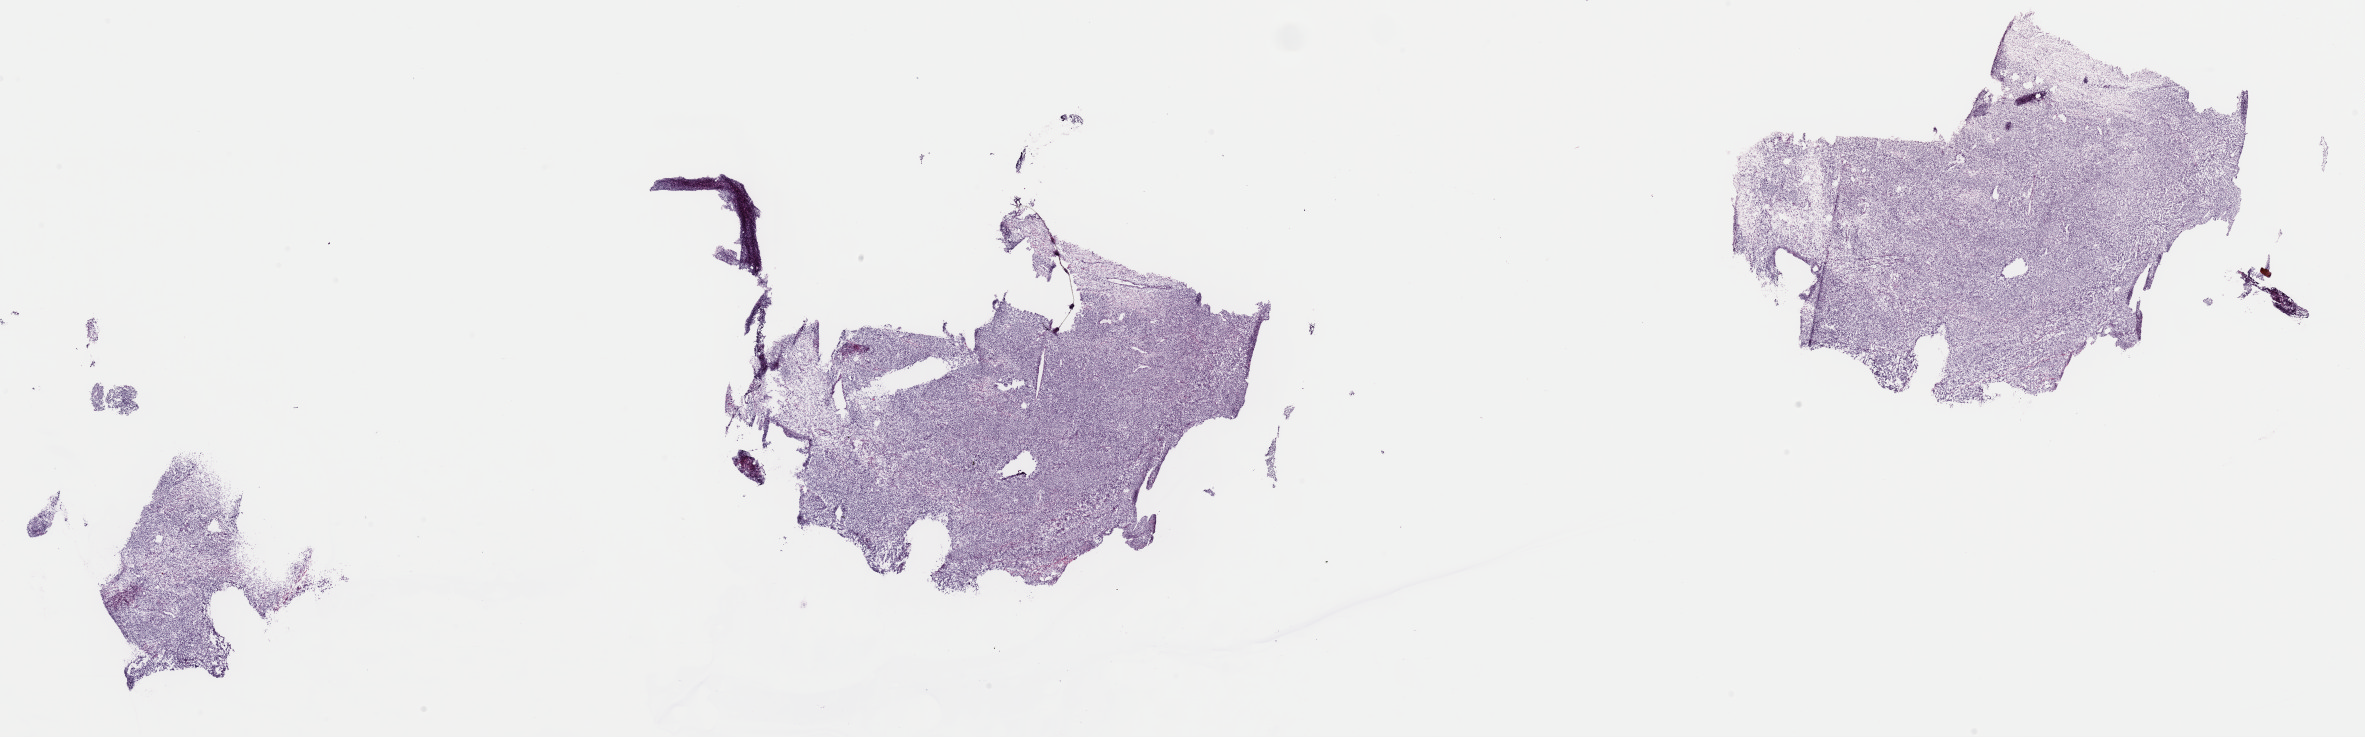
H&E-stained whole-slide image — low-resolution overview of the scanned area, about 37.4 x 11.6 mm (from a 40x scan); frozen section from the top of the tissue portion; primary tumour sample from the connective, subcutaneous and other soft tissues. Female patient; age at initial diagnosis 34 years. Slide review estimates, as recorded: tumour cells 100%, tumour nuclei 80%, normal cells 0%, stromal cells 0%, necrosis 0%. Infiltration values recorded for this section: lymphocyte infiltration 1%, monocyte infiltration 0%, neutrophil infiltration 0%.
• pathologic diagnosis: Malignant peripheral nerve sheath tumor